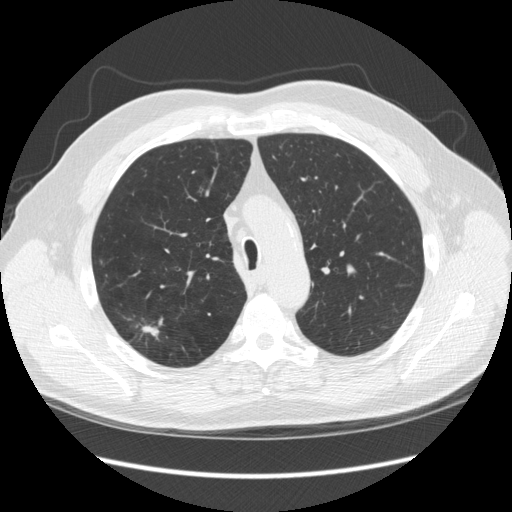
Chest CT (low-dose screening protocol), one axial image. Third screening round (two years after baseline). Lung window (W 1500 / L -600 HU). 2.5 mm slice thickness. Slice 67 of 248 in the series. 512 × 512 image matrix. Male, age 64 years at enrolment.
- Expert-annotated lung lesion, bounding box (x1, y1, x2, y2) in pixels: (117, 314, 170, 358).
- The screening reader recorded 4 non-calcified nodules or masses ≥4 mm on this exam; which of them this box marks is not recorded.
- Official screen result: positive, other.